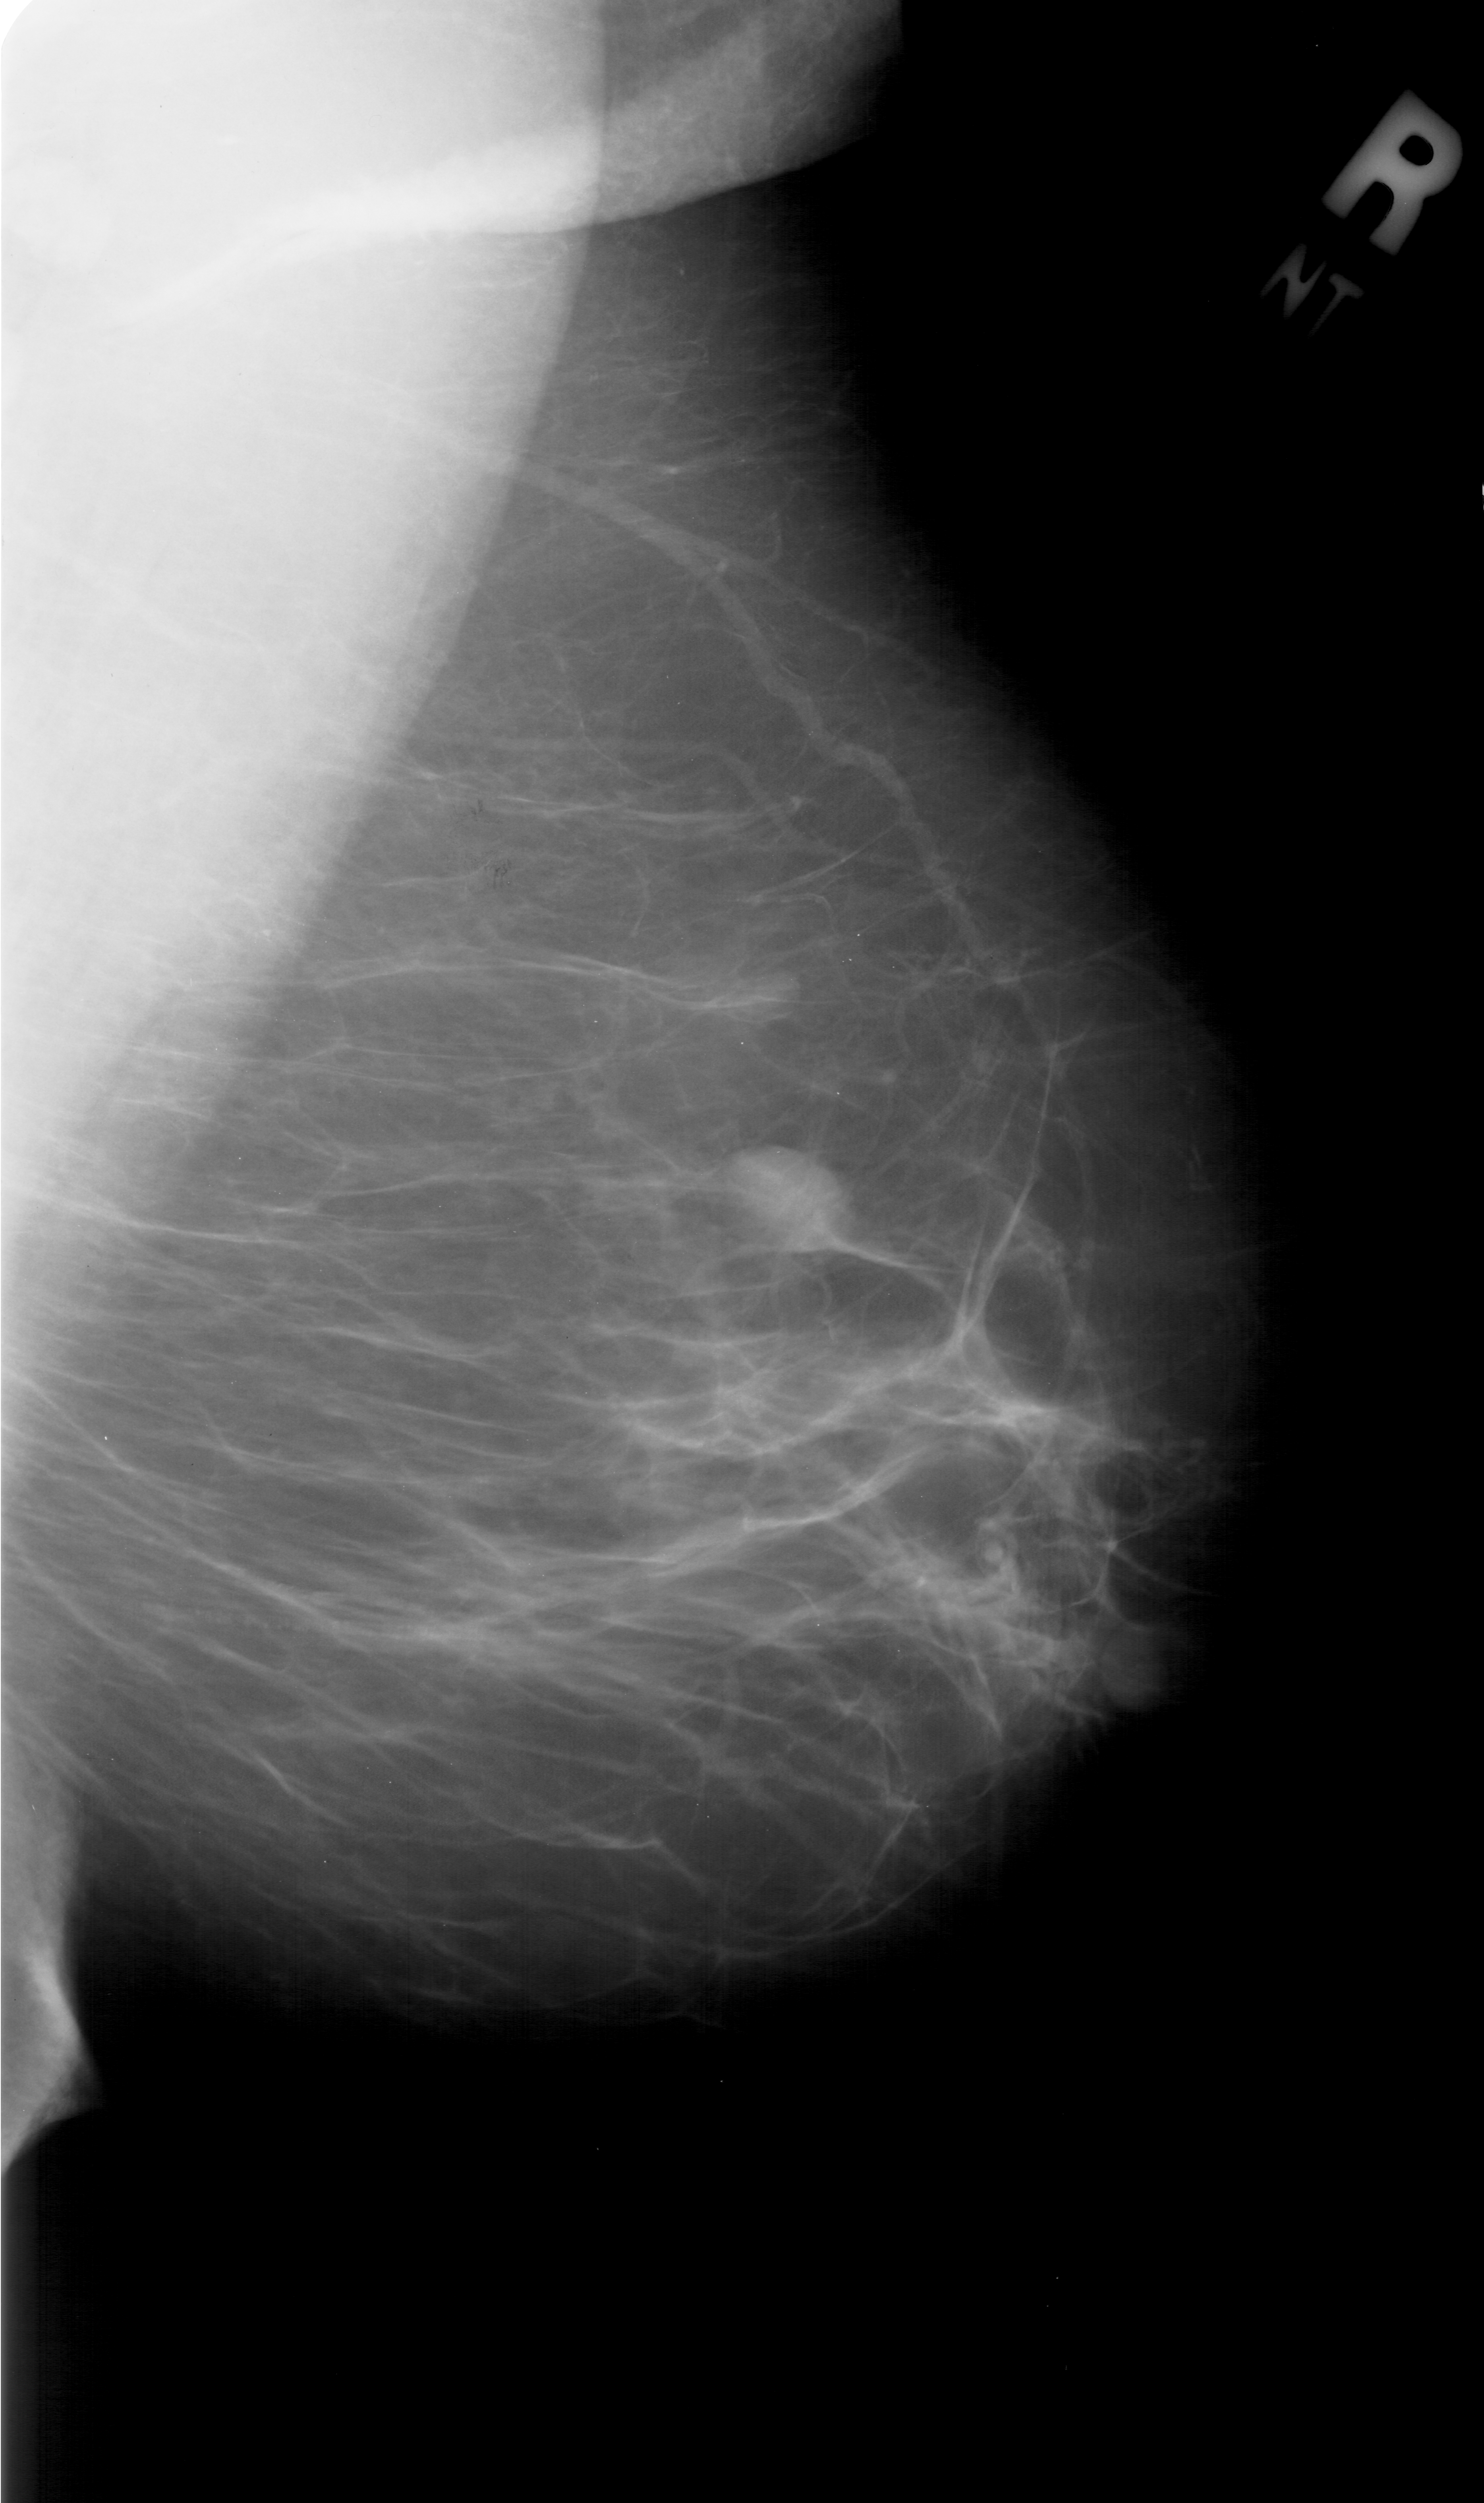
Scanned film-screen mammogram; right breast; MLO view; BI-RADS breast density category 1 (scale 1–4).
- Radiologist-marked abnormalities on this image: mass, shape oval, margins obscured; BI-RADS assessment category 4; pathology (as recorded): benign.